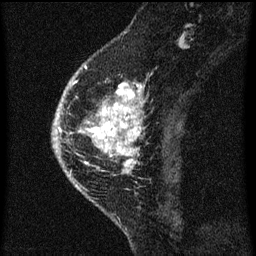
Breast MRI (dynamic contrast-enhanced), one sagittal slice. Slice 22 of 60 in the series (ordered by position). Dynamic contrast-enhanced series, image 2 of 3 at this slice position (ordered by acquisition). 1.5 T. TE 4.2 ms, TR 8 ms. 256 × 256 image matrix, field of view 180 × 180 mm. Female patient, age 46 years.
Annotated regions visible in this slice (semi-automatic segmentation, software-assisted and operator-edited):
- analysis volume of interest (the breast-tissue region the enhancement analysis was run in; not a lesion): bounding box <61,68,145,195> (left, top, right, bottom; pixels)
- tumour enhancement mask (voxels above the 70 % enhancement threshold inside the analysis volume of interest): <78,68,145,175>